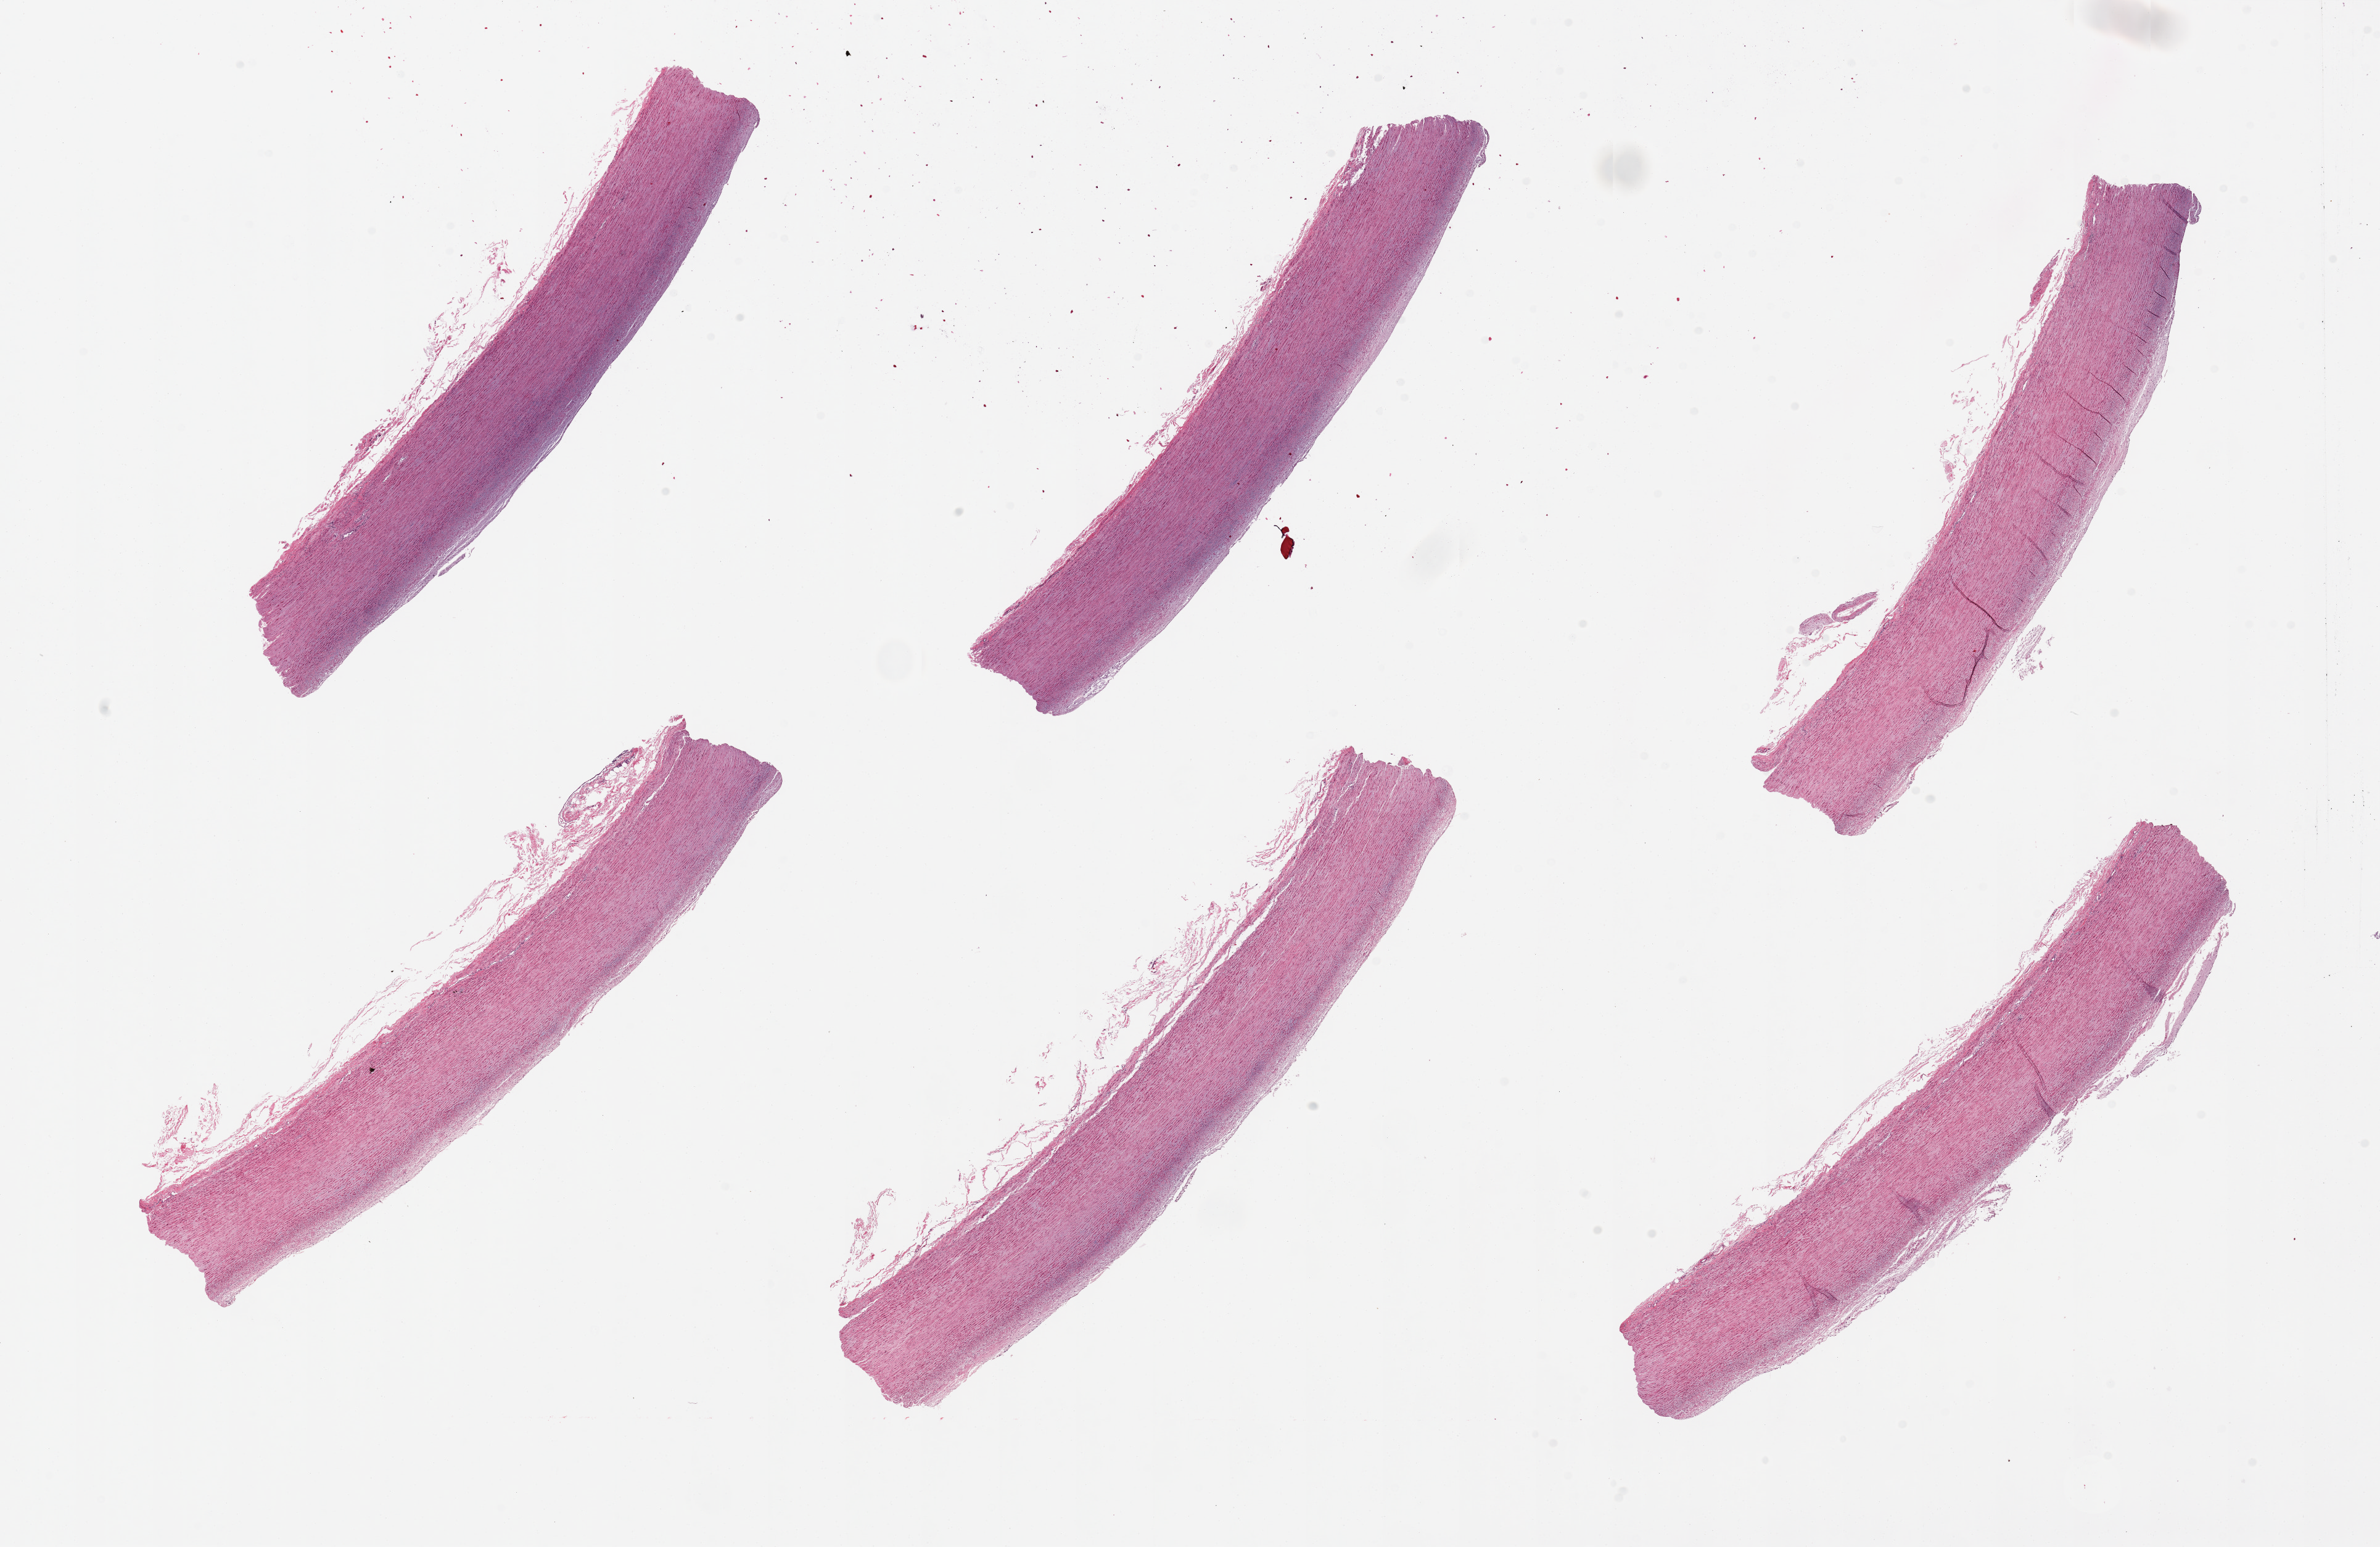
Digitized hematoxylin and eosin (H&E)-stained section, whole scanned area (about 30.5 x 19.8 mm) shown as a low-resolution overview. PAXgene-fixed, paraffin-embedded tissue. Target tissue: aorta. Donor tissue sample. Female donor.
Reviewer comment on this tissue sample: 6 pieces, up to 10x3mm; ~0.2mm layer discontinuous atherosis.